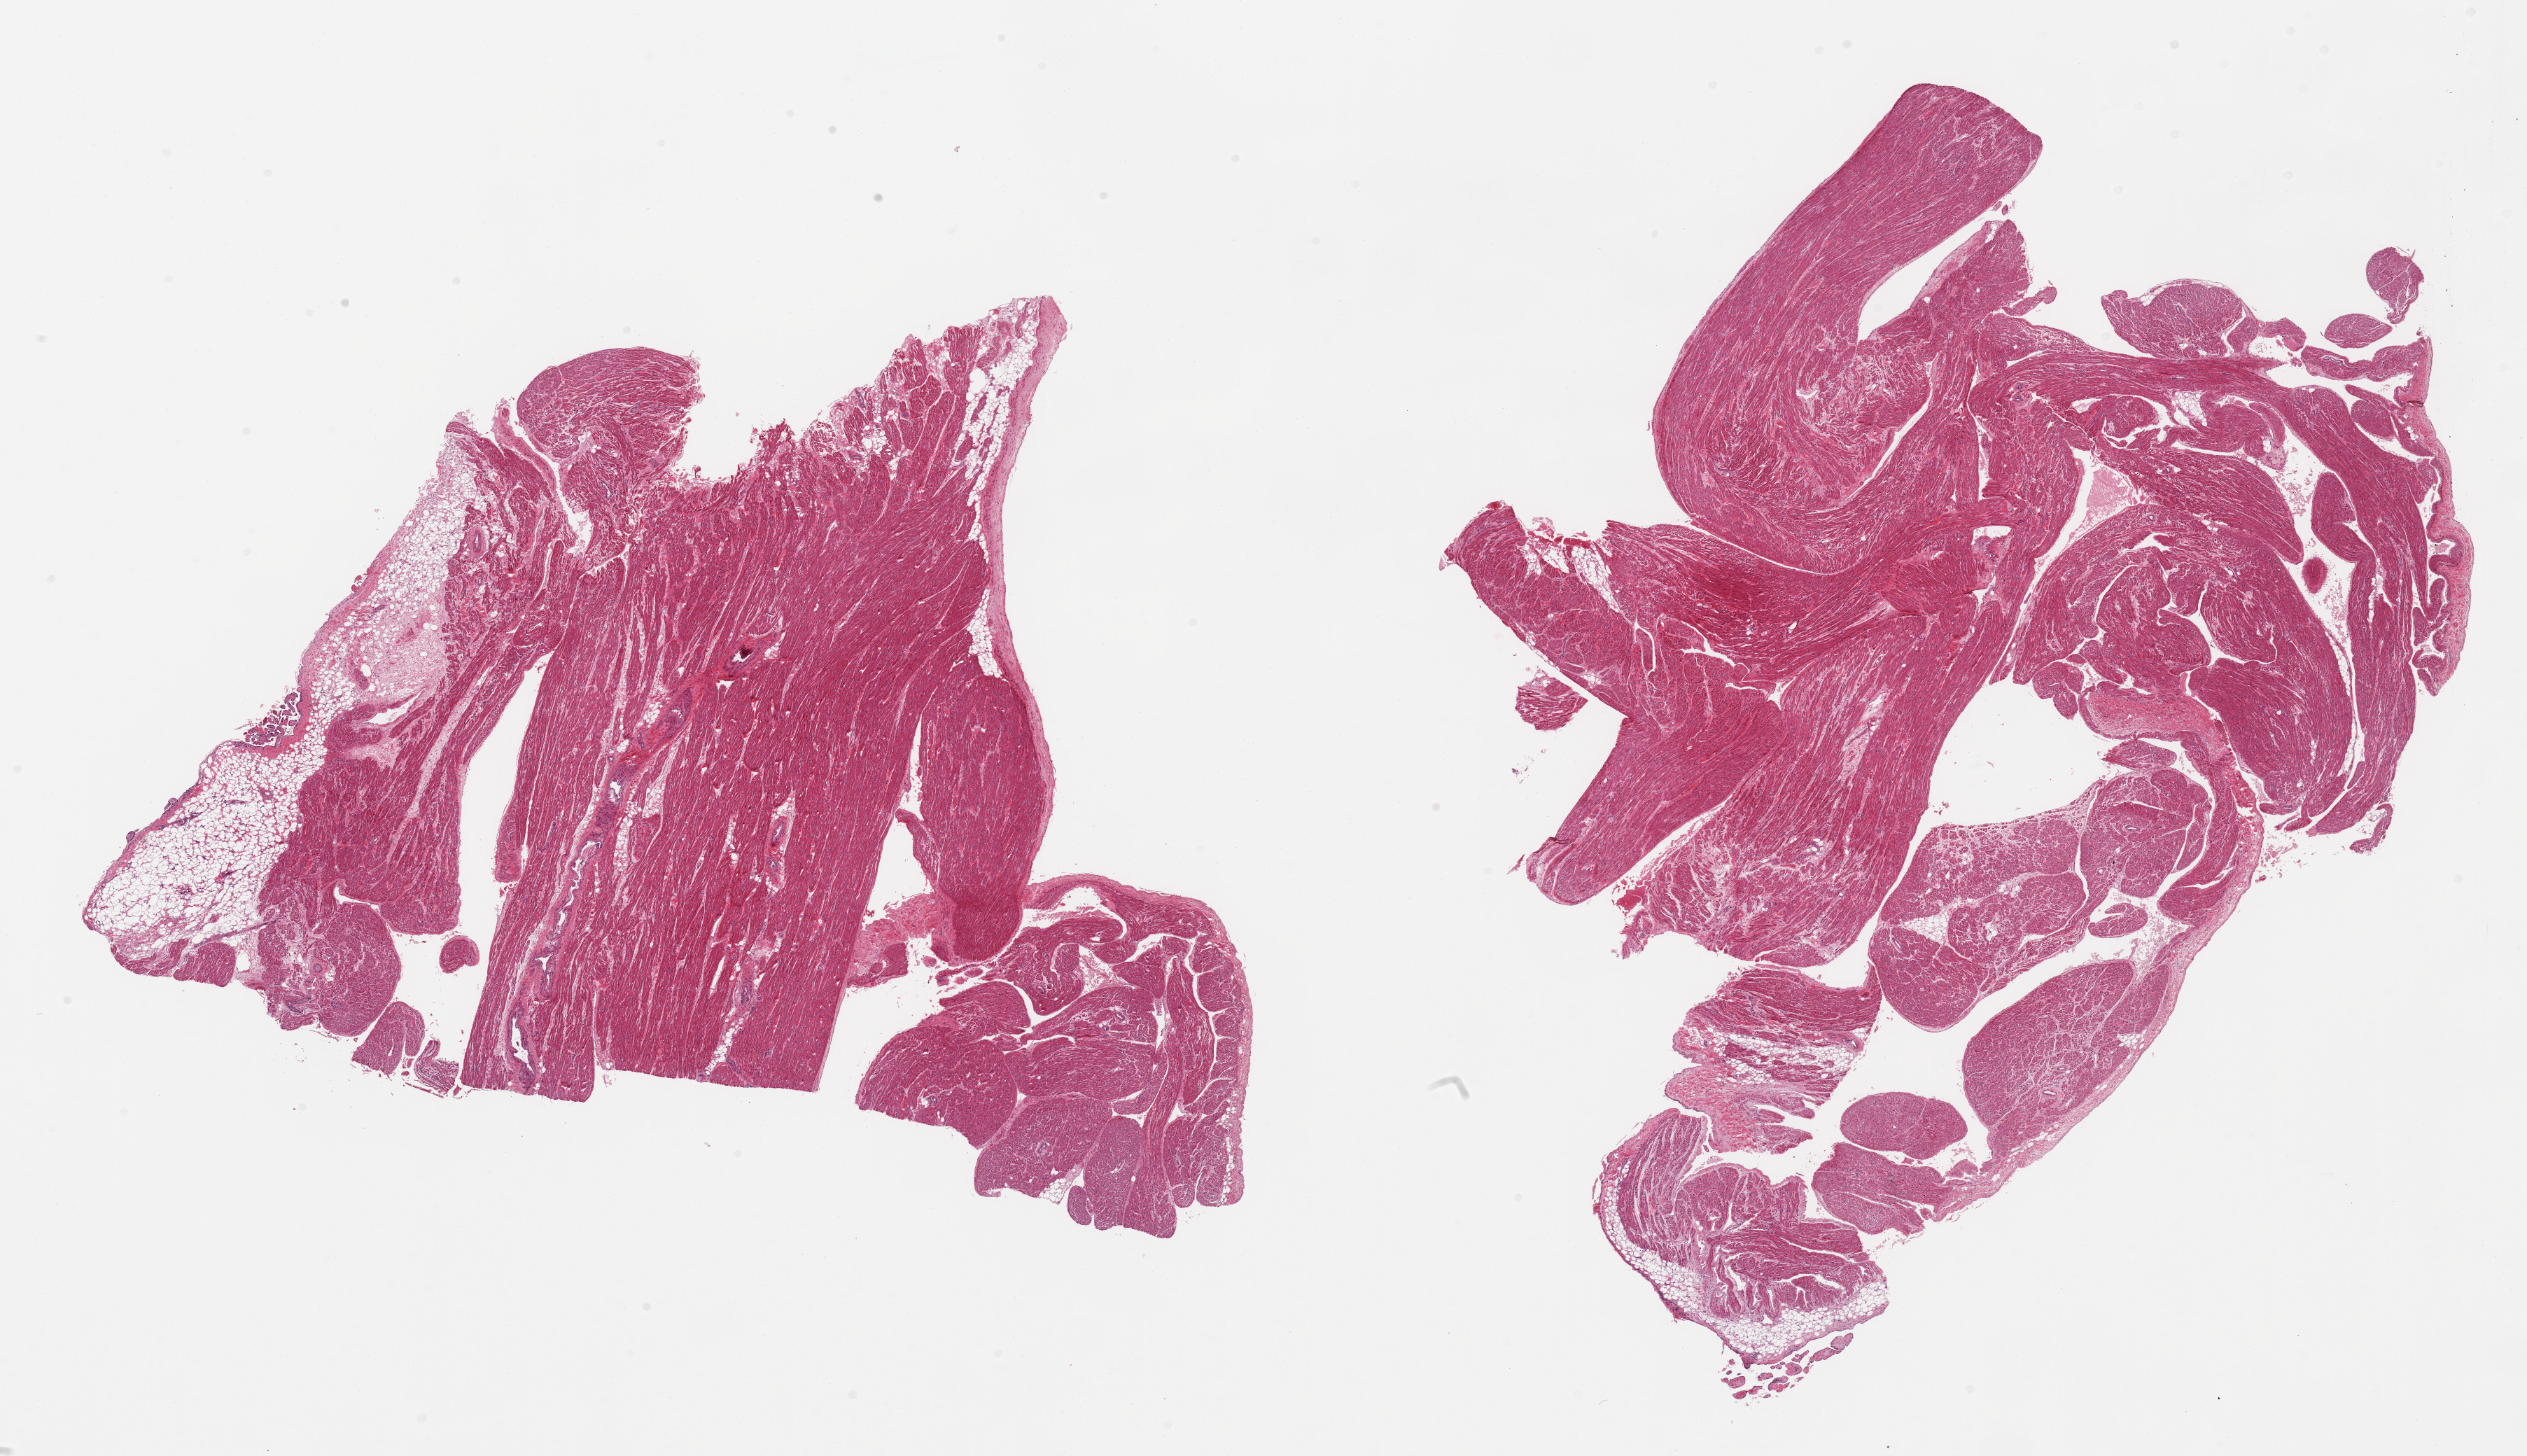
Digitized haematoxylin and eosin-stained section — a low-resolution overview of the entire scanned area, about 28.5 x 16.4 mm (acquisition: 20x scan); PAXgene-fixed, paraffin-embedded tissue; target tissue: auricular appendage; tissue donor sample.
Pathologist's review note for this sample: 2 pieces, no abnormalities.